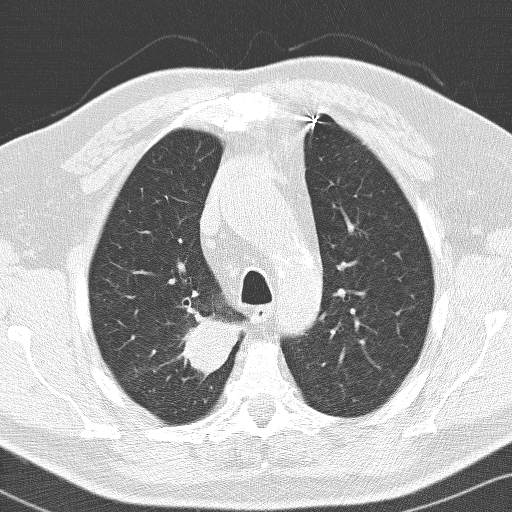
Chest CT (low-dose screening protocol), one axial image. Baseline screening round. Lung window (W 1500 / L -600 HU). Lung (sharp) reconstruction kernel (D). Slice 33 of 141 in the series. Male, age 66 years at enrolment. Former smoker at enrolment.
Expert reader's lesion annotation, bounding box <150,306,231,392> (left, top, right, bottom; pixels). Reader record for this screening exam (exam-level; its link to the box is not recorded): non-calcified nodule or mass ≥4 mm, right upper lobe, 36 × 30 mm, spiculated (stellate) margins, soft tissue attenuation.